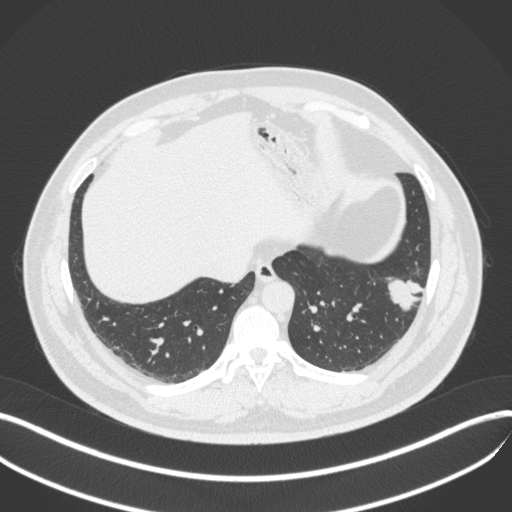
Chest CT, one axial slice. Slice 116 of 420 in the series (ordered by position). Reconstruction kernel B31f. 120 kVp. Lung window (W 1500 / L -600 HU). 1 mm slice thickness. 512 × 512 image matrix. Patient: male, 39 years. From the clinical record (not read from this slice): clinical TNM (as recorded): T2a N0 M0; histopathological grade: G2-3.
Annotated regions visible in this slice (bounding box drawn by a radiologist):
- lung tumour (recorded histology: adenocarcinoma): box from (x=381, y=269) to (x=430, y=316) px